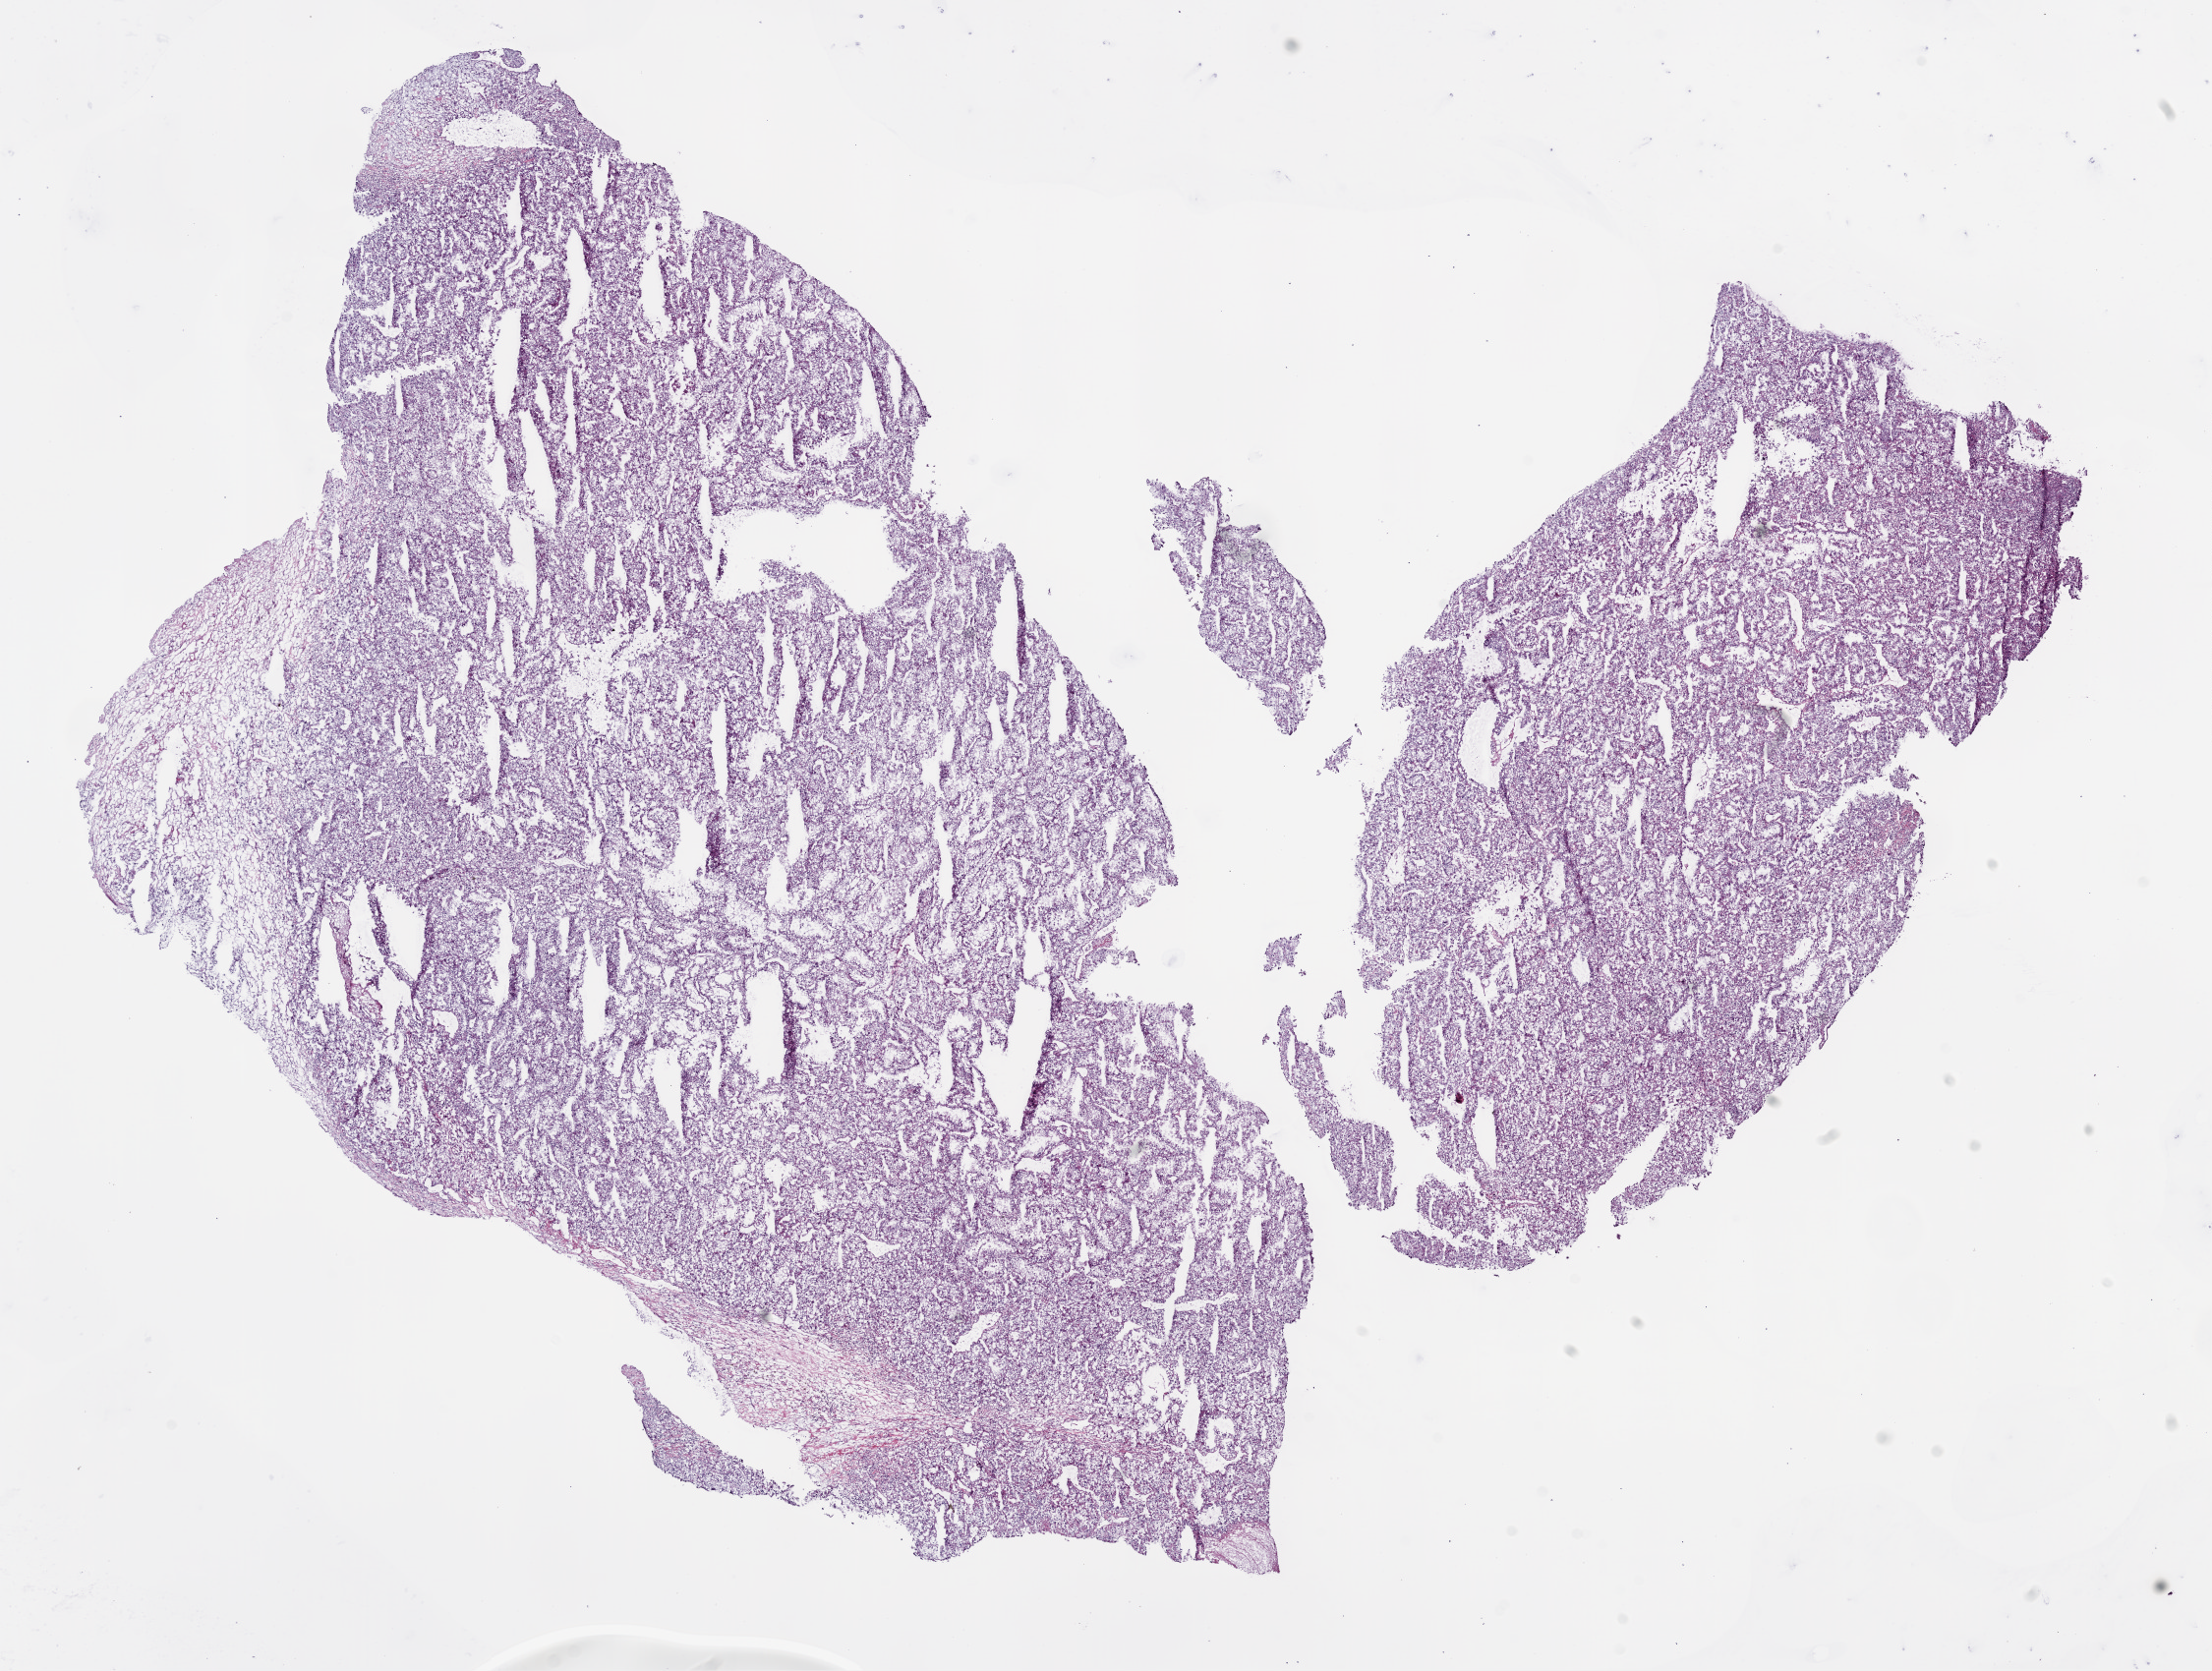
H&E-stained whole-slide image — low-resolution overview of the scanned area, about 18.1 x 13.6 mm (from a 20x scan). Frozen section from the bottom of the tissue portion. Kidney, primary tumour sample. Male patient; age at initial diagnosis 60 years. Histologic grade: G3 (poorly differentiated). Composition of this section per pathologist review: tumour cells 90%, tumour nuclei 90%, normal cells 0%, stromal cells 10%, necrosis 0%.
Laterality: right. Pathologic diagnosis: Clear cell adenocarcinoma, NOS. TNM: T1a NX M0. AJCC pathologic stage: I.